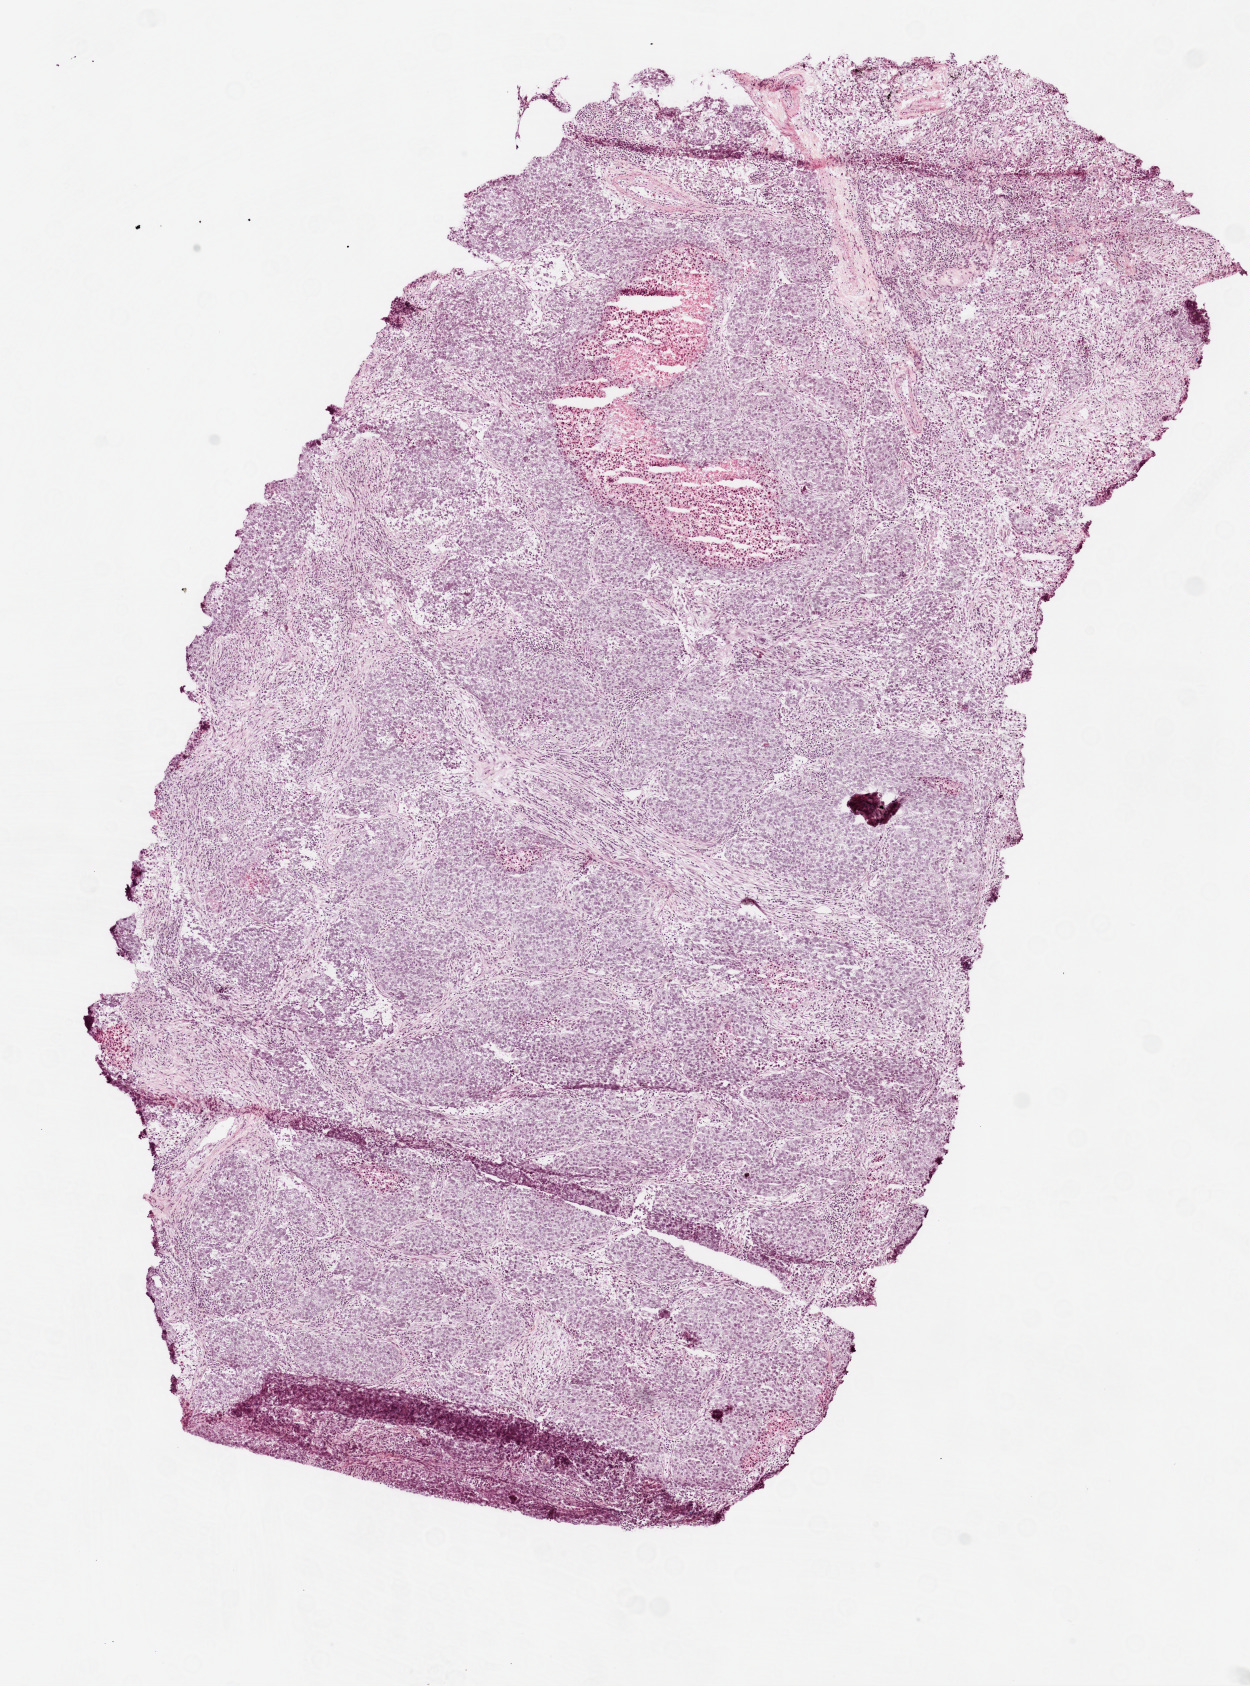
H&E whole-slide image — whole scanned area (about 5.0 x 6.8 mm, from a 20x scan) shown as a low-resolution overview, frozen section, lung, primary tumour sample. Patient: male, age at initial diagnosis 58 years. Slide review estimates, as recorded: tumour cells 85%, tumour nuclei 85%, normal cells 0%, stromal cells 5%, necrosis 10%.
Histologic diagnosis: Squamous cell carcinoma, NOS. AJCC pathologic stage: IA.